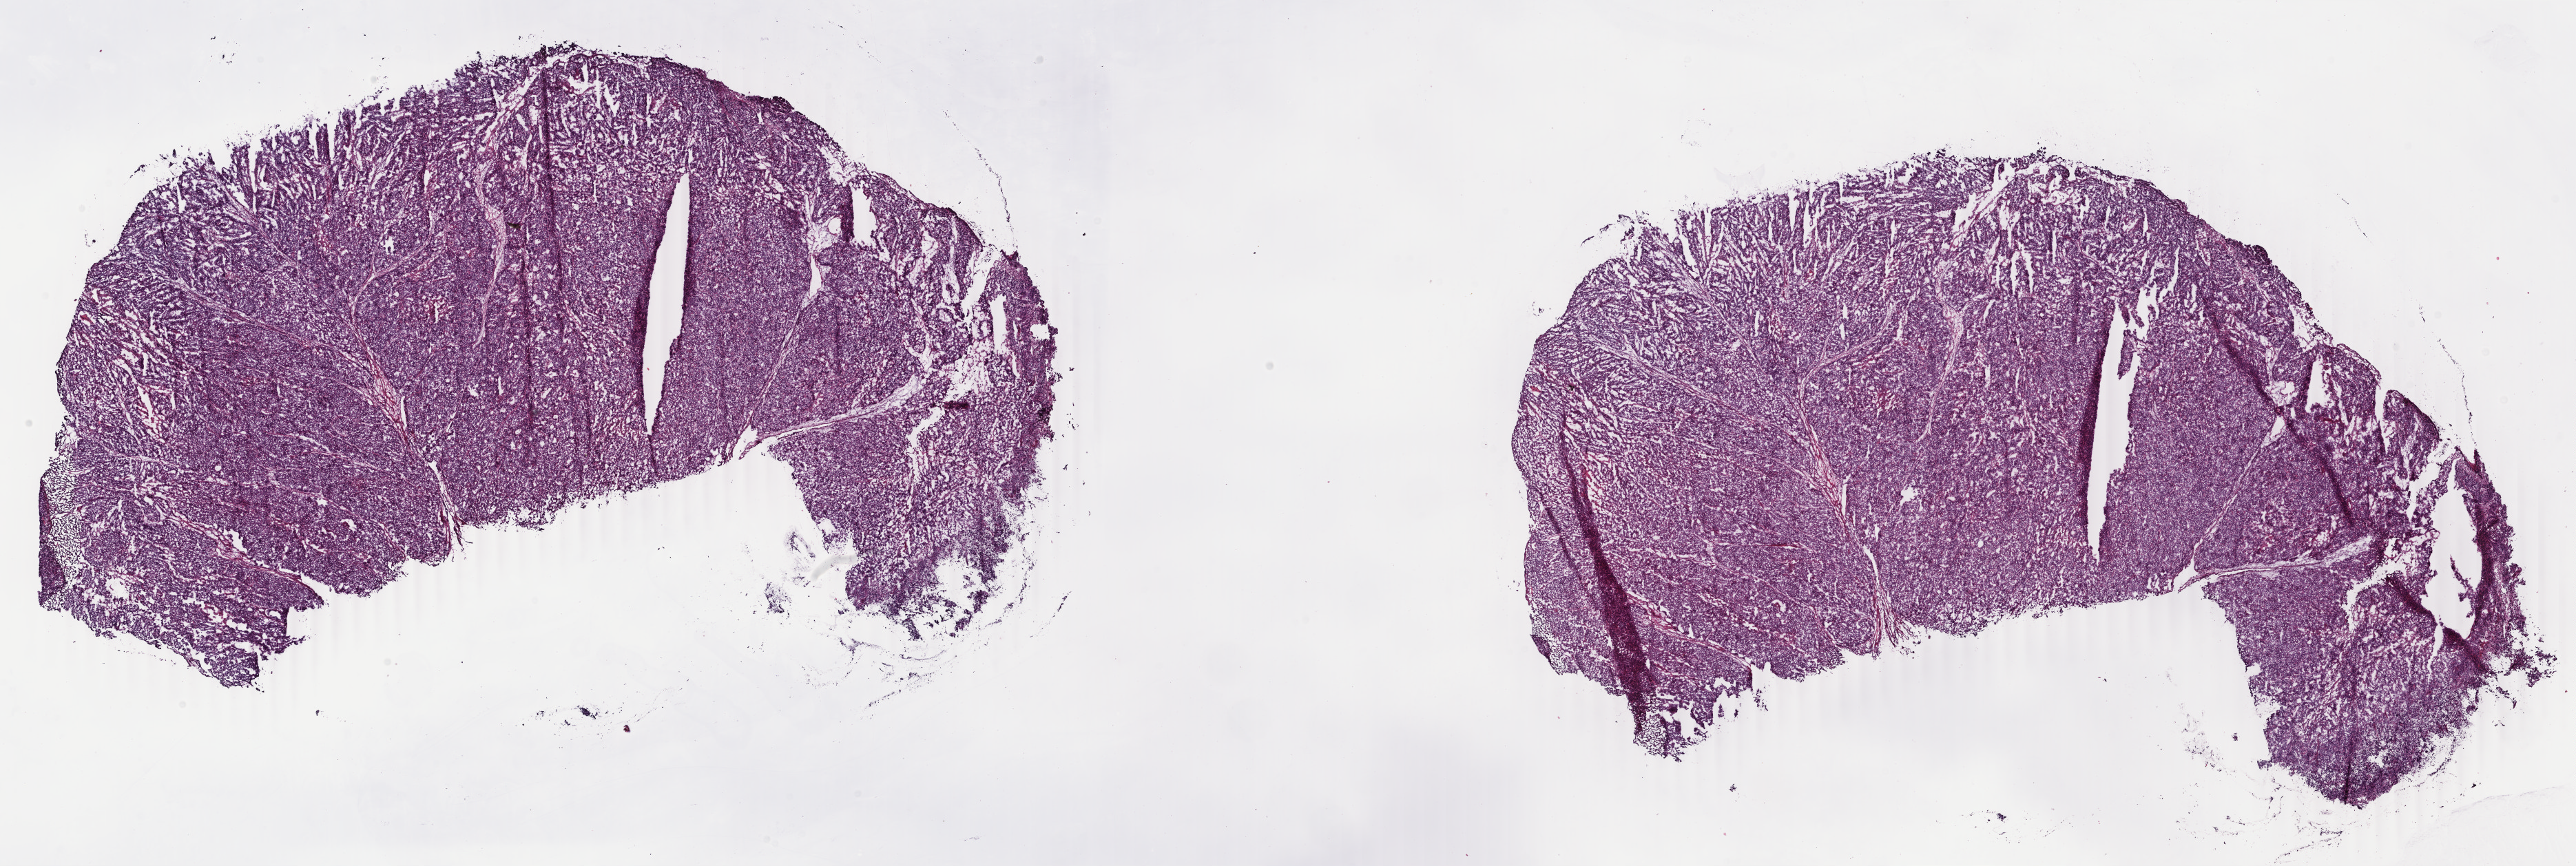
Digitized H&E-stained tissue section (whole slide), whole scanned area (about 29.7 x 10.0 mm, slide scanned at 40x) shown as a low-resolution overview. Frozen section from the bottom of the tissue portion. Primary tumour sample from the uterus. Patient sex: female. Histologic grade: G3 (poorly differentiated). Composition of this section per pathologist review: tumour cells 83%, tumour nuclei 98%, normal cells 0%, stromal cells 2%, necrosis 15%. Infiltration values recorded for this section: lymphocyte infiltration 0%, monocyte infiltration 0%, neutrophil infiltration 0%.
FIGO stage: IA. Histologic diagnosis: Endometrioid adenocarcinoma, NOS. Lymph nodes positive (case pathology): 0 of 3 examined.